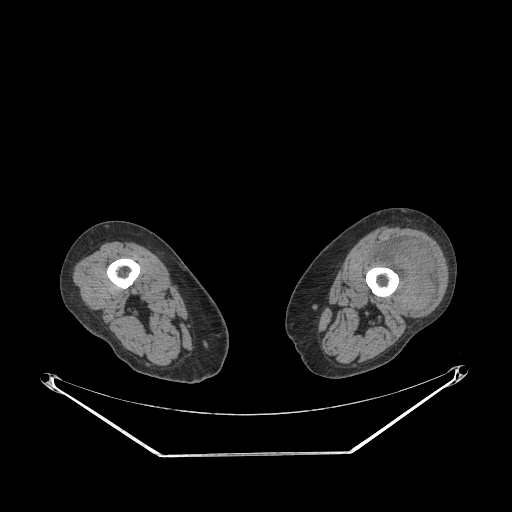
CT of an extremity soft-tissue mass (from a PET/CT study), one axial slice; position 204 of 267 along the scan axis; 140 kVp; soft-tissue window (W 400 / L 40 HU); 3.75 mm slice thickness; 512 × 512 image matrix, field of view 500 × 500 mm. Female patient. From the clinical record (not read from this slice): histological type: undifferentiated – high grade; grade: high; site of the primary tumour: left thigh.
Outlined on this slice (expert contour drawn on MRI and transferred to this co-registered scan by the dataset authors):
- gross tumour volume including surrounding oedema: bounding box (x1, y1, x2, y2) in pixels: (370, 238, 435, 314)
- gross tumour volume (mass): (399, 246, 433, 314)